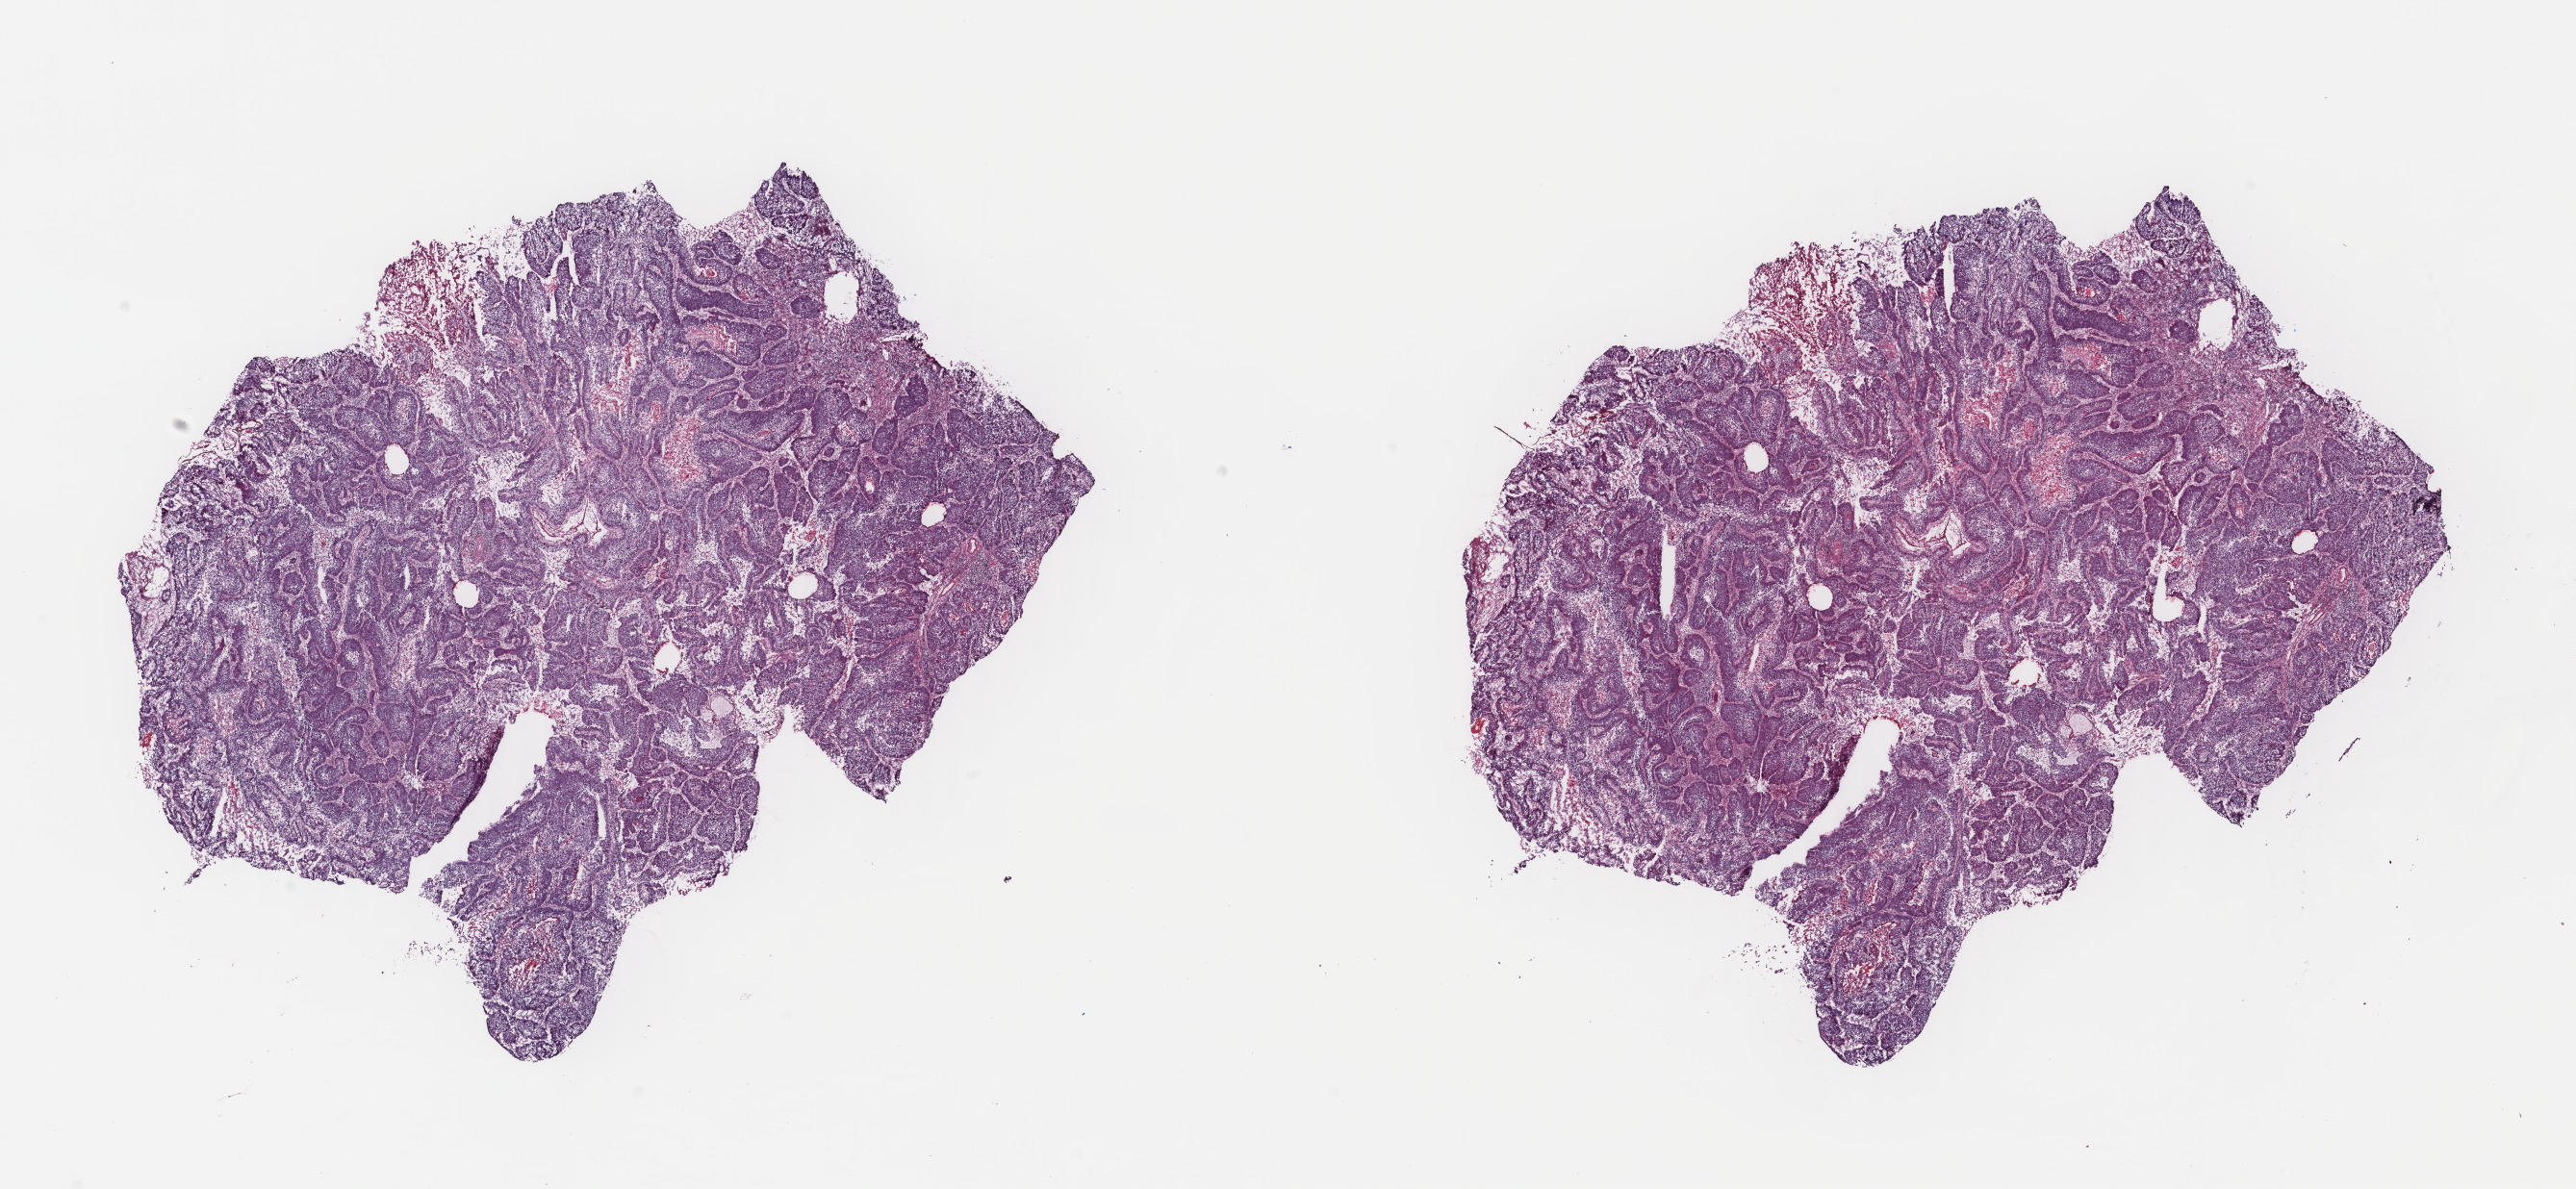
H&E-stained whole-slide image — shown as a low-resolution overview of the whole scanned area (about 21.2 x 9.8 mm). Frozen section. Sample: primary tumour, cervix. Female patient; age at initial diagnosis 29 years. Slide review estimates, as recorded: tumour cells 70%, tumour nuclei 70%.
Diagnosis: Squamous cell carcinoma, keratinizing, NOS.